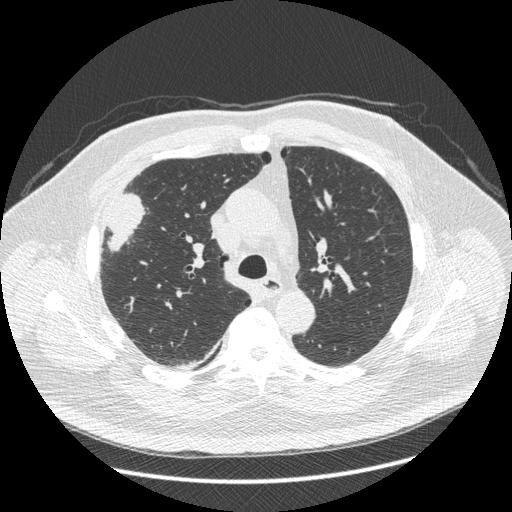
Low-dose screening chest CT, one axial slice; reconstruction kernel STANDARD; lung window (W 1500 / L -600 HU); 1.25 mm slice thickness; 512 × 512 image matrix, field of view 400 × 400 mm.
Annotated regions visible in this slice (expert manual segmentation):
- lesion 1 (tumor, upper lobe of right lung): box from (x=107, y=193) to (x=145, y=251) px